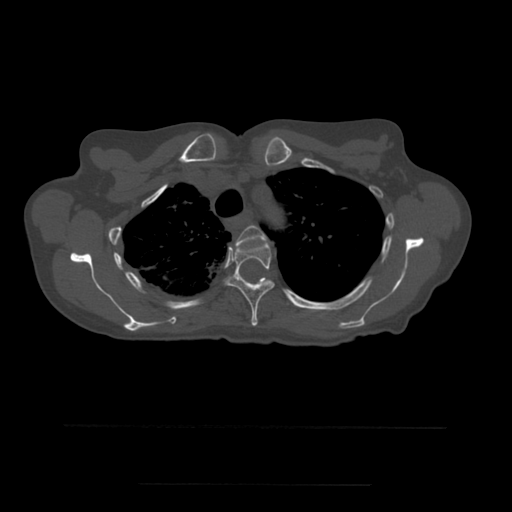
CT including the spine, one axial slice; position 408 of 544 along the scan axis; bone window (W 1800 / L 400 HU); 1.25 mm slice thickness; 512 × 512 image matrix. Patient age 58 years. Case-level facts recorded for this patient, not image findings: primary cancer: lung.
Outlined on this slice (semi-automatically segmented with operator editing):
- T3 vertebra: bounding box <236,226,267,247> (left, top, right, bottom; pixels)
- T4 vertebra: <226,241,275,327>